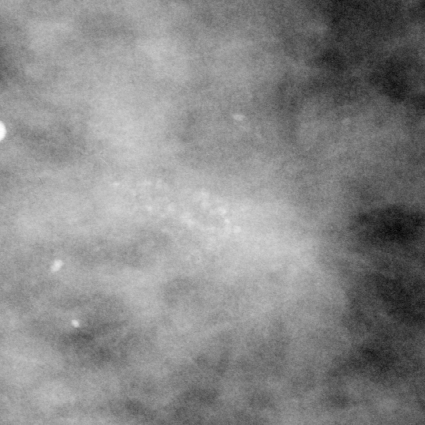
Cropped region of a digitized screen-film mammogram centred on a radiologist-marked abnormality, left breast, CC view, BI-RADS breast density category 2 (scale 1–4).
- Calcifications, morphology amorphous, distribution clustered; BI-RADS assessment category 5; subtlety rating 4 on a 1 (subtle) to 5 (obvious) scale; pathology (as recorded): malignant.